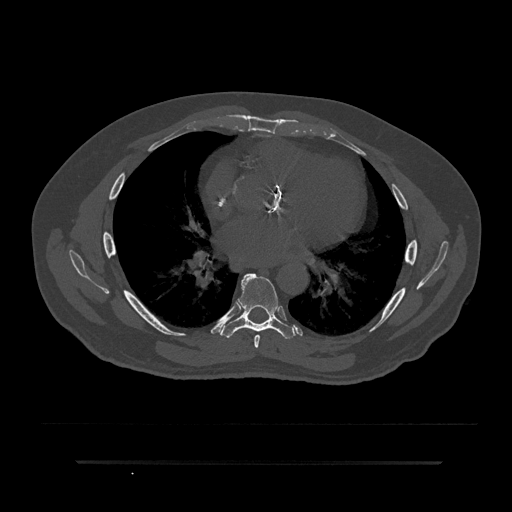
CT including the spine, one axial slice; position 489 of 797 along the scan axis; reconstruction kernel Br40s/3; 120 kVp; bone window (W 1800 / L 400 HU); 512 × 512 image matrix, field of view 464 × 464 mm. Patient: male, 59 years. From the clinical record (not read from this slice): primary cancer: bile ducts; vertebrae with lytic lesions (as recorded): T10.
Annotated regions visible in this slice (semi-automatically segmented with operator editing):
- T6 vertebra: box from (x=254, y=335) to (x=260, y=348) px
- T7 vertebra: (x=220, y=273)–(x=295, y=339)